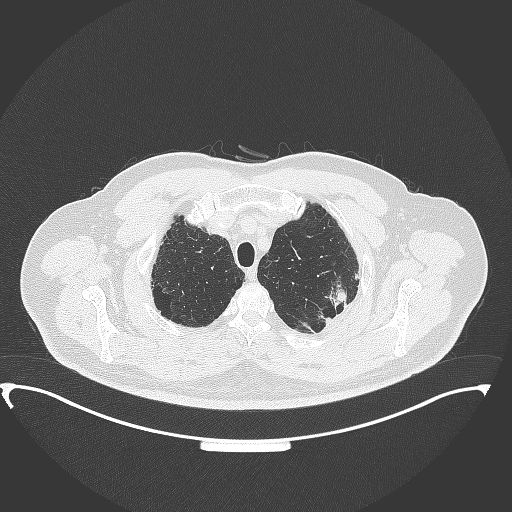
Chest CT, one axial slice. Position 312 of 350 along the scan axis. Reconstruction kernel B70f. 120 kVp. Lung window (W 1500 / L -600 HU). 512 × 512 image matrix. Male patient, age 64 years. From the clinical record (not read from this slice): clinical TNM (as recorded): T1c N1 M1.
Structures marked on this image (bounding box drawn by a radiologist):
- lung tumour (recorded histology: adenocarcinoma): box from (x=325, y=275) to (x=352, y=315) px